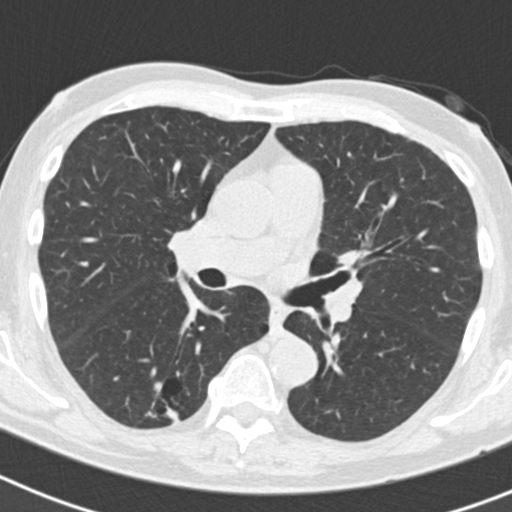
Chest CT (low-dose screening protocol), one axial image. Second annual screen. Lung window (W 1500 / L -600 HU). Standard (soft-tissue) reconstruction kernel (B30f). Slice 77 of 186 in the series. Male, age 70 years at enrolment. Current smoker at enrolment.
• Lesion marked by an expert reader, bounding box <132,375,198,433> (left, top, right, bottom; pixels).
• The screening reader recorded 5 non-calcified nodules or masses ≥4 mm on this exam (right lower lobe, right lower lobe, right upper lobe, right upper lobe, left upper lobe); which of them this box marks is not recorded.
• Official screen result: positive, other.
• Later outcome: lung cancer diagnosed 622 days after this screen (after the third annual screen) — bronchiolo-alveolar adenocarcinoma, NOS, right lower lobe, poorly differentiated (G3), stage IB (AJCC 6th edition), 30 mm at pathology.